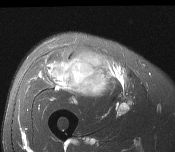
MRI of an extremity soft-tissue mass, one axial slice. T2-weighted fat-saturated. MR volume resampled by the dataset authors to the PET/CT grid (not the native acquisition matrix). 3.27 mm slice thickness. 175 × 152 image matrix. Male patient. Case-level facts recorded for this patient, not image findings: histological type: pleiomorphic leiomyosarcoma; grade: intermediate; site of the primary tumour: right thigh.
Outlined on this slice (expert contour drawn on MRI and transferred to this co-registered scan by the dataset authors):
- gross tumour volume including surrounding oedema: bounding box [x1, y1, x2, y2] px = [49, 49, 112, 98]
- gross tumour volume (mass): [49, 52, 112, 98]